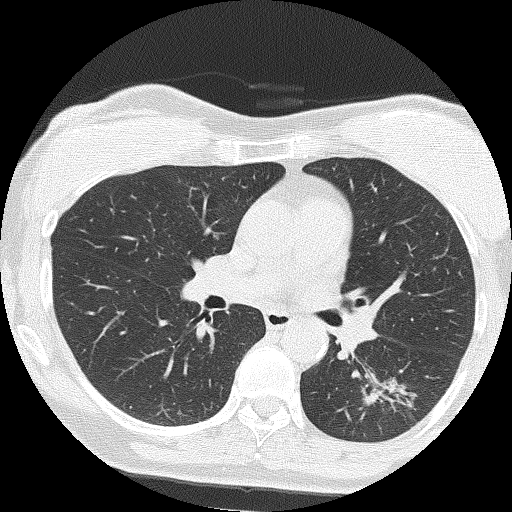
Low-dose screening chest CT, axial slice, second screening round (one year after baseline), lung window (W 1500 / L -600 HU), 2 mm slice thickness, lung (sharp) reconstruction kernel (FC51), slice 70 of 159 in the series. Female, age 64 years at enrolment. Former smoker at enrolment.
Expert reader's lesion annotation, bounding box [x1, y1, x2, y2] px = [359, 365, 444, 438]. The screening reader recorded 3 non-calcified nodules or masses ≥4 mm on this exam (right upper lobe, right upper lobe, right middle lobe); which of them this box marks is not recorded. Participant outcome: lung cancer diagnosed 576 days after this screen — adenocarcinoma, NOS, left lower lobe, moderately differentiated (G2), stage IA (AJCC 6th edition), 17 mm at pathology.